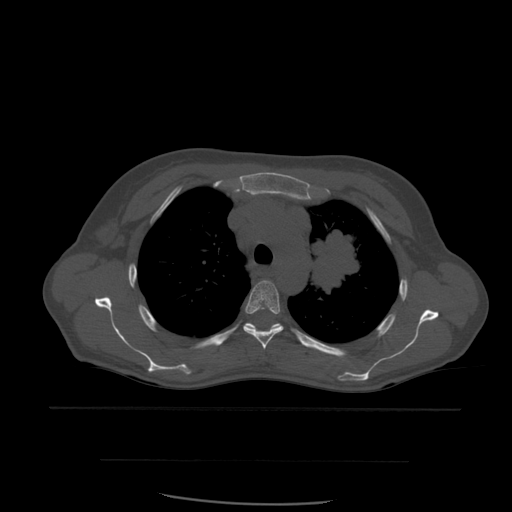
CT including the spine, one axial slice. Slice 424 of 574 in the series (ordered by position). Bone window (W 1800 / L 400 HU). 512 × 512 image matrix, field of view 392 × 392 mm. Patient age 48 years. From the clinical record (not read from this slice): primary cancer: lung; vertebrae with lytic lesions (as recorded): T11.
Outlined on this slice (semi-automatically segmented with operator editing):
- T4 vertebra: bounding box [x1, y1, x2, y2] px = [244, 281, 284, 350]
- T5 vertebra: [244, 323, 282, 329]